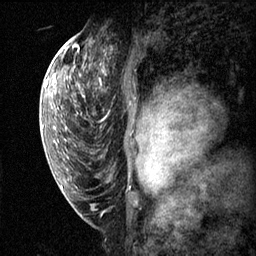
Breast MRI (dynamic contrast-enhanced), one sagittal slice; slice 41 of 60 in the series (ordered by position); dynamic contrast-enhanced series, image 2 of 3 at this slice position (ordered by acquisition); 1.5 T; TE 4.2 ms, TR 11.1 ms; 256 × 256 image matrix. Female patient, age 50 years.
Structures marked on this image (semi-automatic segmentation, software-assisted and operator-edited):
- analysis volume of interest (the breast-tissue region the enhancement analysis was run in; not a lesion): bounding box (x1, y1, x2, y2) in pixels: (82, 56, 164, 143)
- tumour enhancement mask (voxels above the 70 % enhancement threshold inside the analysis volume of interest): (142, 116, 164, 143)